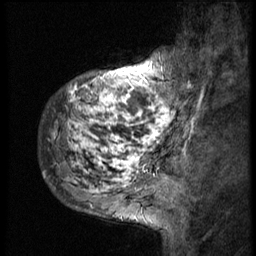
Breast MRI (dynamic contrast-enhanced), one sagittal slice. Position 11 of 58 along the scan axis. 3 images stored at this slice position (order not interpretable as contrast timing). 1.5 T. TE 4.2 ms, TR 9 ms. 2.5 mm slice thickness. 256 × 256 image matrix. Female patient, age 50 years. Case-level facts recorded for this patient, not image findings: setting: breast cancer imaged before/during neoadjuvant chemotherapy; receptor status: triple-negative.
Structures marked on this image (semi-automatic segmentation, software-assisted and operator-edited):
- analysis volume of interest (the breast-tissue region the enhancement analysis was run in; not a lesion): bounding box (x1, y1, x2, y2) in pixels: (40, 48, 186, 214)
- tumour enhancement mask (voxels above the 140 % enhancement threshold inside the analysis volume of interest): (53, 65, 177, 192)